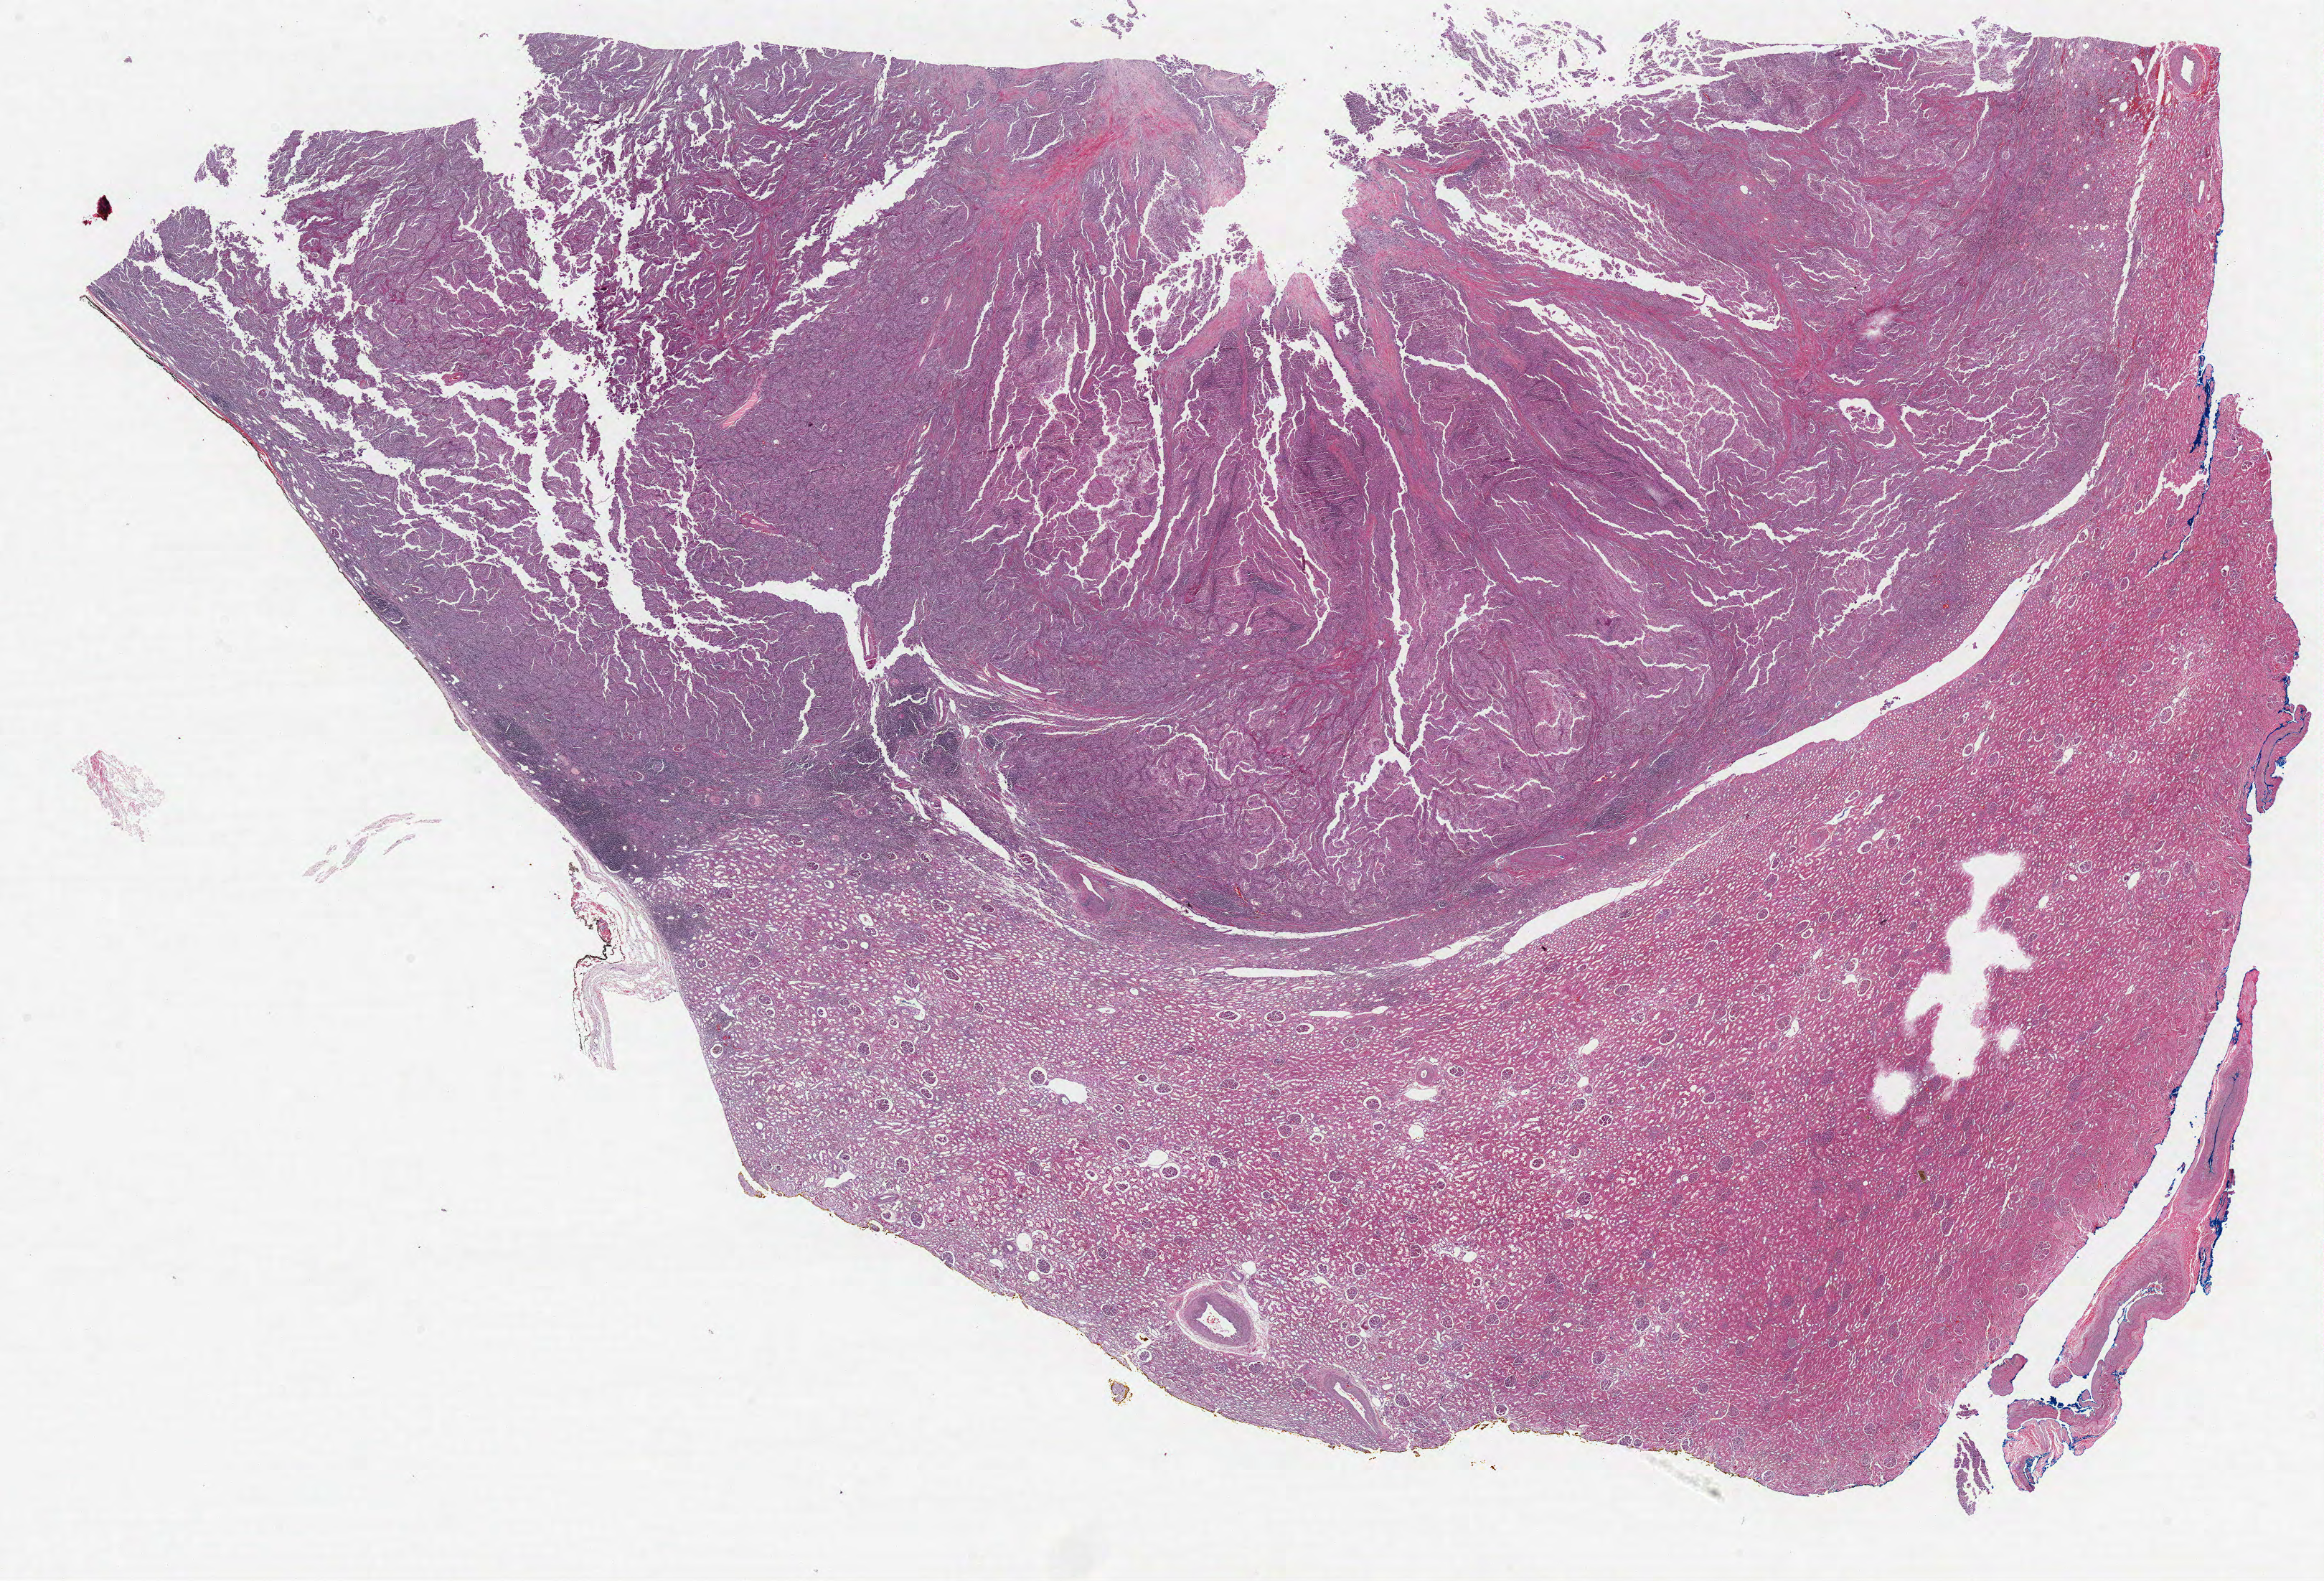
Digitized H&E tissue section (whole slide) — whole scanned area (about 25.9 x 17.6 mm, slide scanned at 40x) shown as a low-resolution overview; formalin-fixed paraffin-embedded (FFPE) diagnostic section; primary tumour sample from the kidney. Patient: female, age at initial diagnosis 45 years.
• laterality: right
• diagnosis: Papillary adenocarcinoma, NOS
• AJCC pathologic stage: I